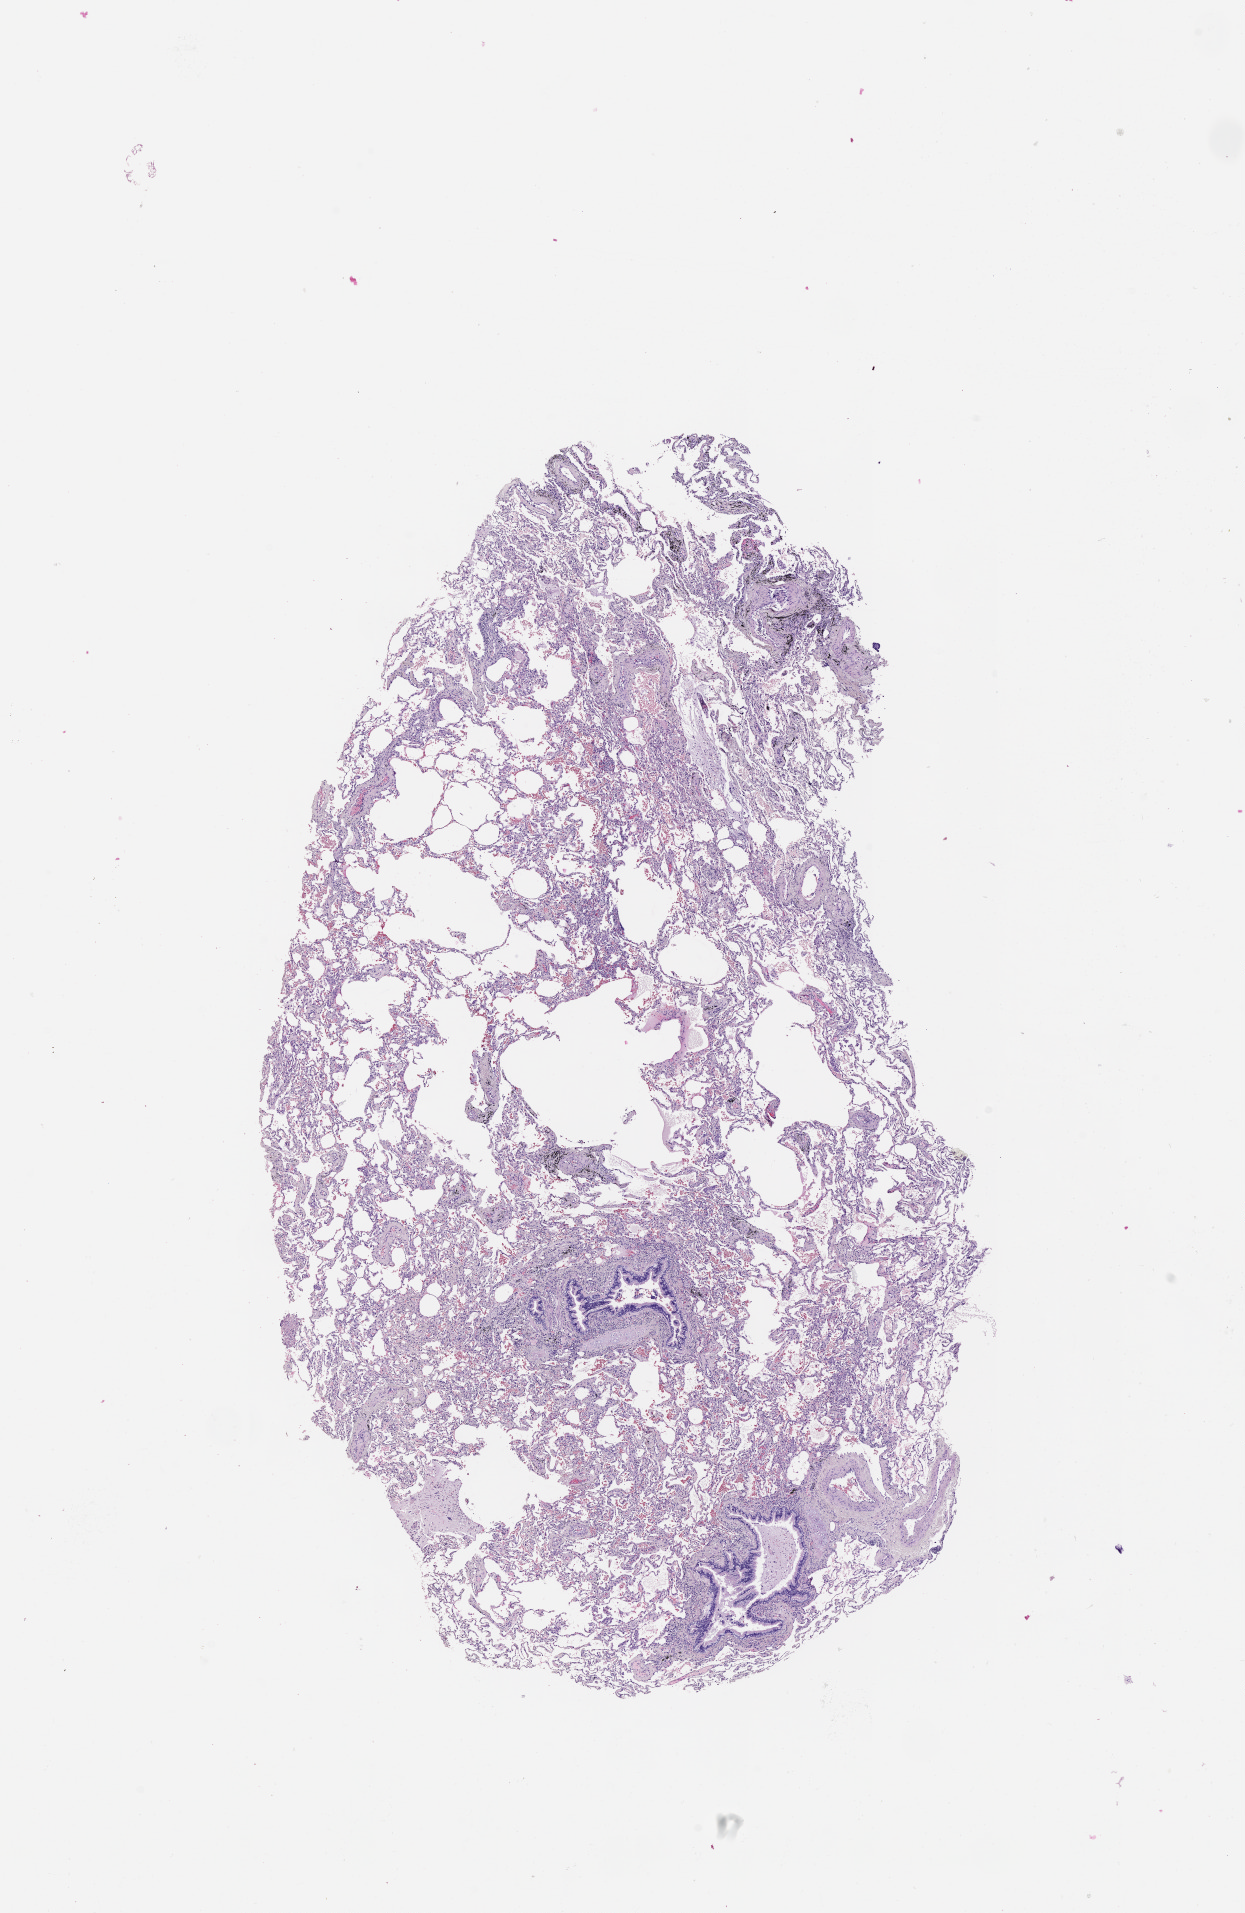
Whole-slide histology image, H&E — shown as a low-resolution overview of the whole scanned area (about 10.0 x 15.4 mm), normal (non-tumour) tissue sample, lung. Male, 60 y/o.
• this section: normal (non-tumour) tissue from the same patient
• patient diagnosis (cohort enrolment): squamous cell carcinoma (lung)